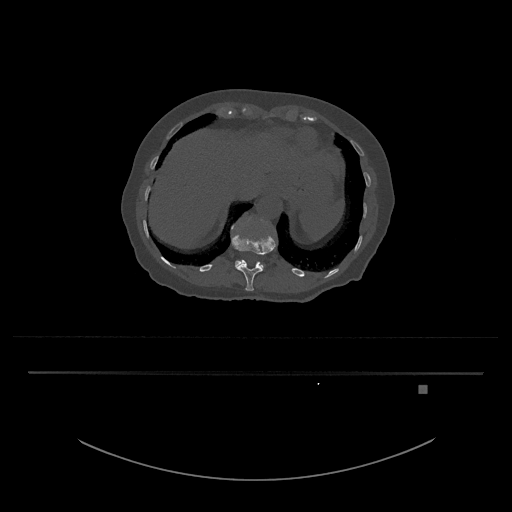
CT including the spine, one axial slice; slice 596 of 797 in the series (ordered by position); reconstruction kernel Br40s/3; 120 kVp; bone window (W 1800 / L 400 HU); 512 × 512 image matrix, field of view 500 × 500 mm. Female patient, age 57 years. From the clinical record (not read from this slice): primary cancer: cervical.
Structures marked on this image (semi-automatic segmentation, software-assisted and operator-edited):
- L1 vertebra: bounding box (x1, y1, x2, y2) in pixels: (235, 260, 265, 269)
- T12 vertebra: (231, 231, 276, 291)